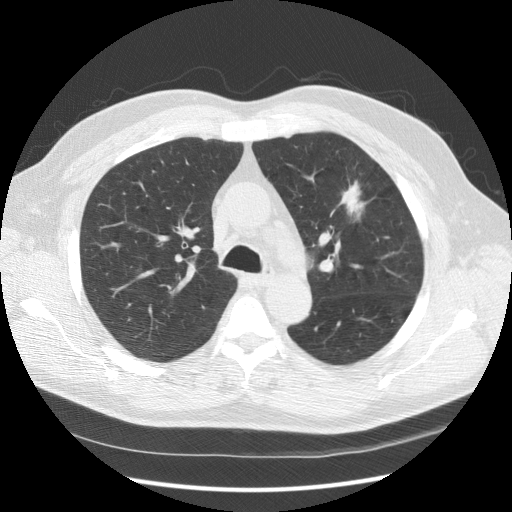
Chest CT (low-dose screening protocol), one axial image; second screening round (one year after baseline); lung window (W 1500 / L -600 HU); slice 52 of 157 in the series. Male, age 65 years at enrolment. Current smoker at enrolment.
• Lesion marked by an expert reader, bounding box [x1, y1, x2, y2] px = [325, 172, 377, 229].
• The screening reader recorded 2 non-calcified nodules or masses ≥4 mm on this exam (left upper lobe, right upper lobe); which of them this box marks is not recorded.
• Later outcome: lung cancer diagnosed 120 days after this screen — carcinoma, NOS, left upper lobe, poorly differentiated (G3), stage IIIA (AJCC 6th edition), 25 mm at pathology.